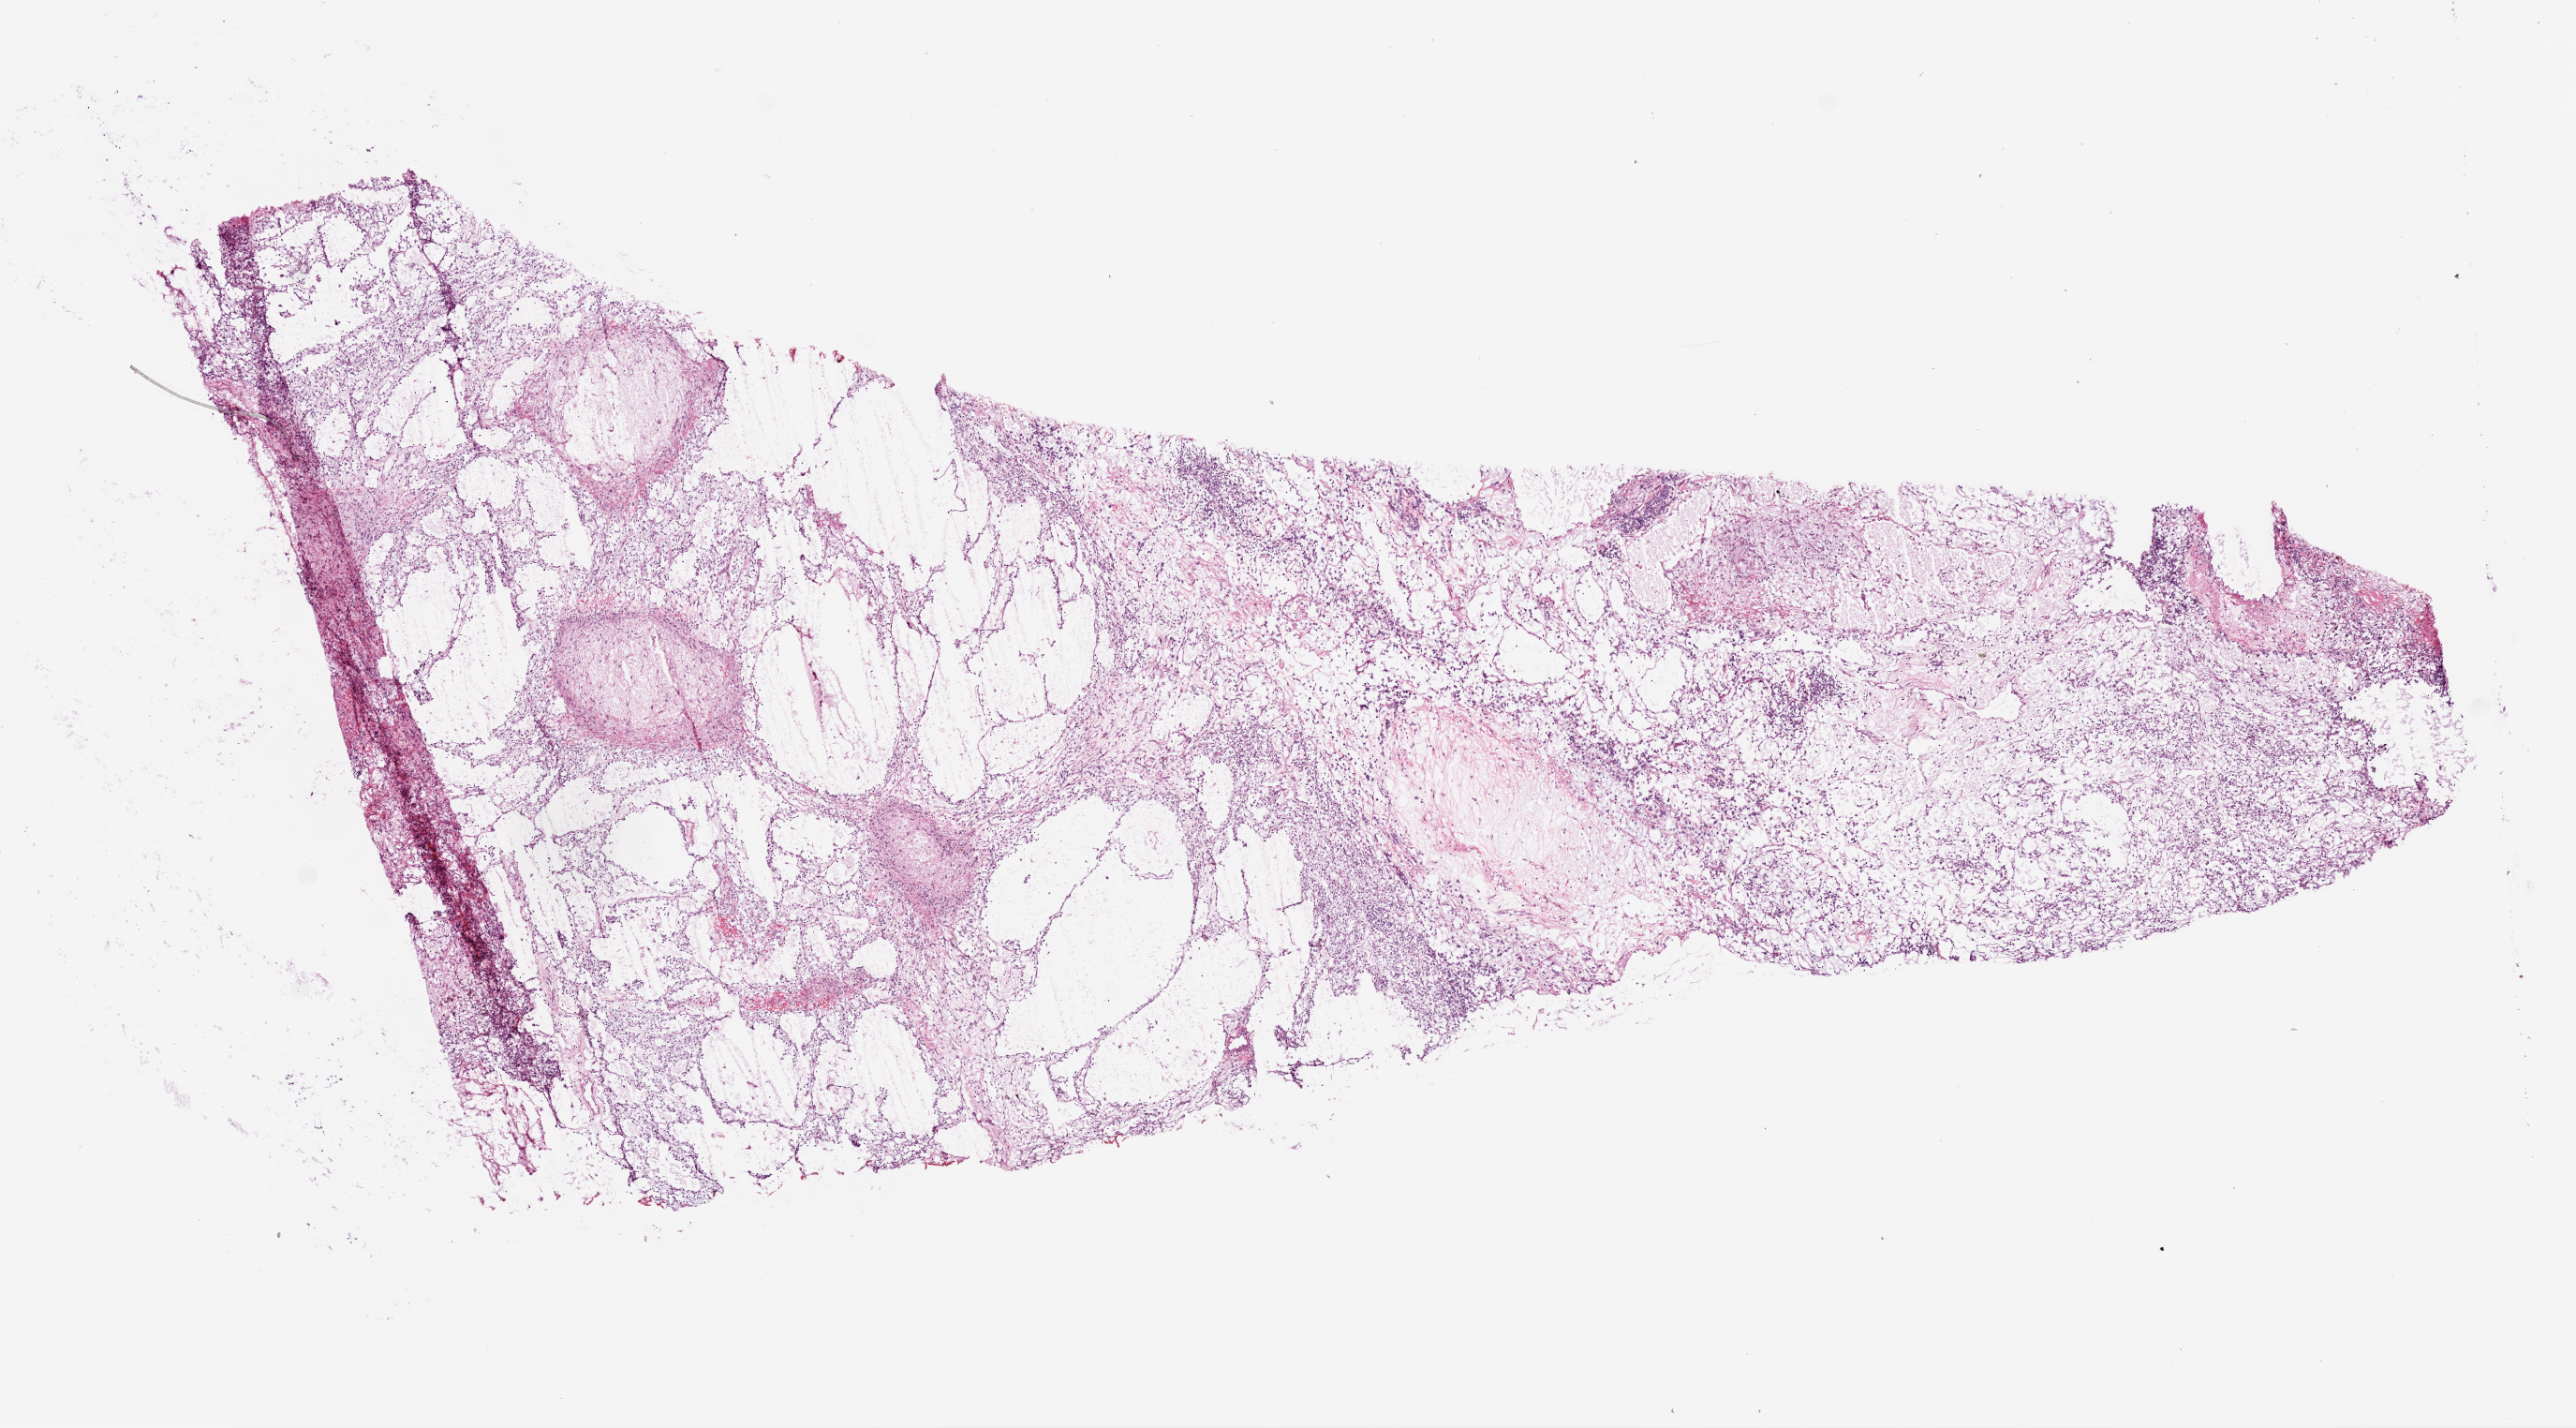
Whole-slide histology image, H&E-stained — whole scanned area (about 11.0 x 6.1 mm, slide scanned at 20x) shown as a low-resolution overview. Frozen section from the bottom of the tissue portion. Kidney, primary tumour sample. Patient: male, age at initial diagnosis 62 years. Histologic grade: G2 (moderately differentiated). Pathologist review of this section (percent, as recorded): tumour cells 90%, tumour nuclei 75%, normal cells 0%, stromal cells 10%, necrosis 0%.
- AJCC pathologic stage: II (7th edition)
- diagnosis: Clear cell adenocarcinoma, NOS
- TNM: T2a NX M0